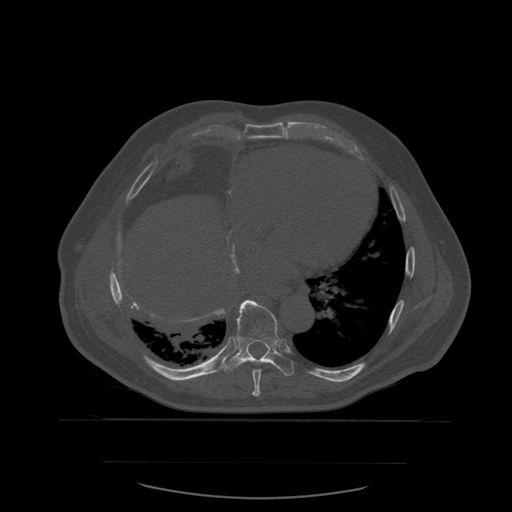
CT including the spine, one axial slice; slice 347 of 590 in the series (ordered by position); bone window (W 1800 / L 400 HU); 1.25 mm slice thickness; 512 × 512 image matrix, field of view 479 × 479 mm. Patient age 71 years. Case-level facts recorded for this patient, not image findings: primary cancer: lung; vertebrae with lytic lesions (as recorded): T1, T2, L5, S1.
Structures marked on this image (semi-automatic segmentation, software-assisted and operator-edited):
- T8 vertebra: bounding box (x1, y1, x2, y2) in pixels: (252, 370, 262, 397)
- T9 vertebra: (220, 300, 295, 377)